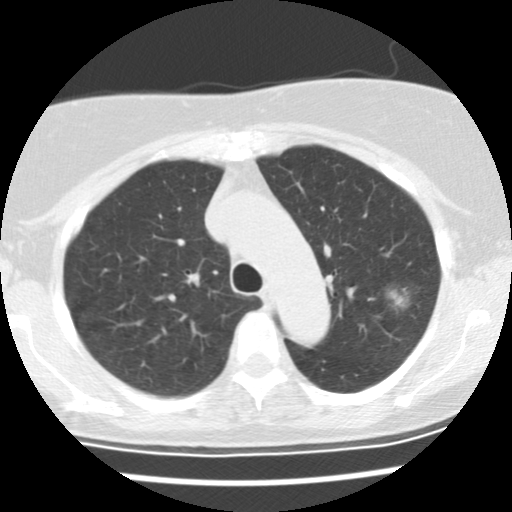
Low-dose screening chest CT, one axial slice; position 103 of 137 along the scan axis; lung window (W 1500 / L -600 HU); 2.5 mm slice thickness; 512 × 512 image matrix, field of view 288 × 288 mm.
Annotated regions visible in this slice (expert manual segmentation):
- lesion 1 (tumor, upper lobe of left lung): bounding box [x1, y1, x2, y2] px = [388, 288, 410, 310]